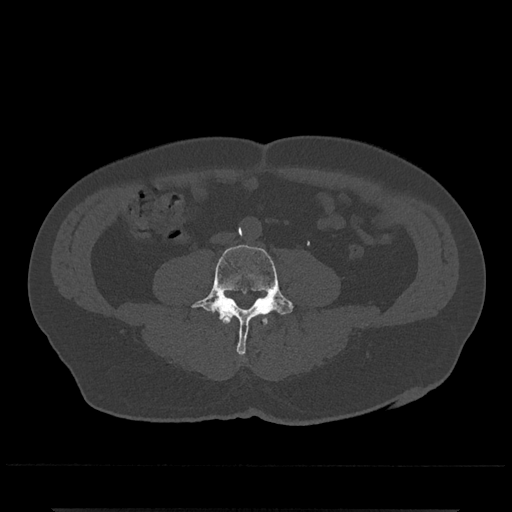
CT including the spine, one axial slice; position 154 of 797 along the scan axis; 120 kVp; bone window (W 1800 / L 400 HU); 512 × 512 image matrix, field of view 393 × 393 mm. Male patient, age 67 years. From the clinical record (not read from this slice): primary cancer: prostate.
Structures marked on this image (semi-automatic segmentation, software-assisted and operator-edited):
- L3 vertebra: bounding box <221,314,268,325> (left, top, right, bottom; pixels)
- L4 vertebra: <191,244,294,356>